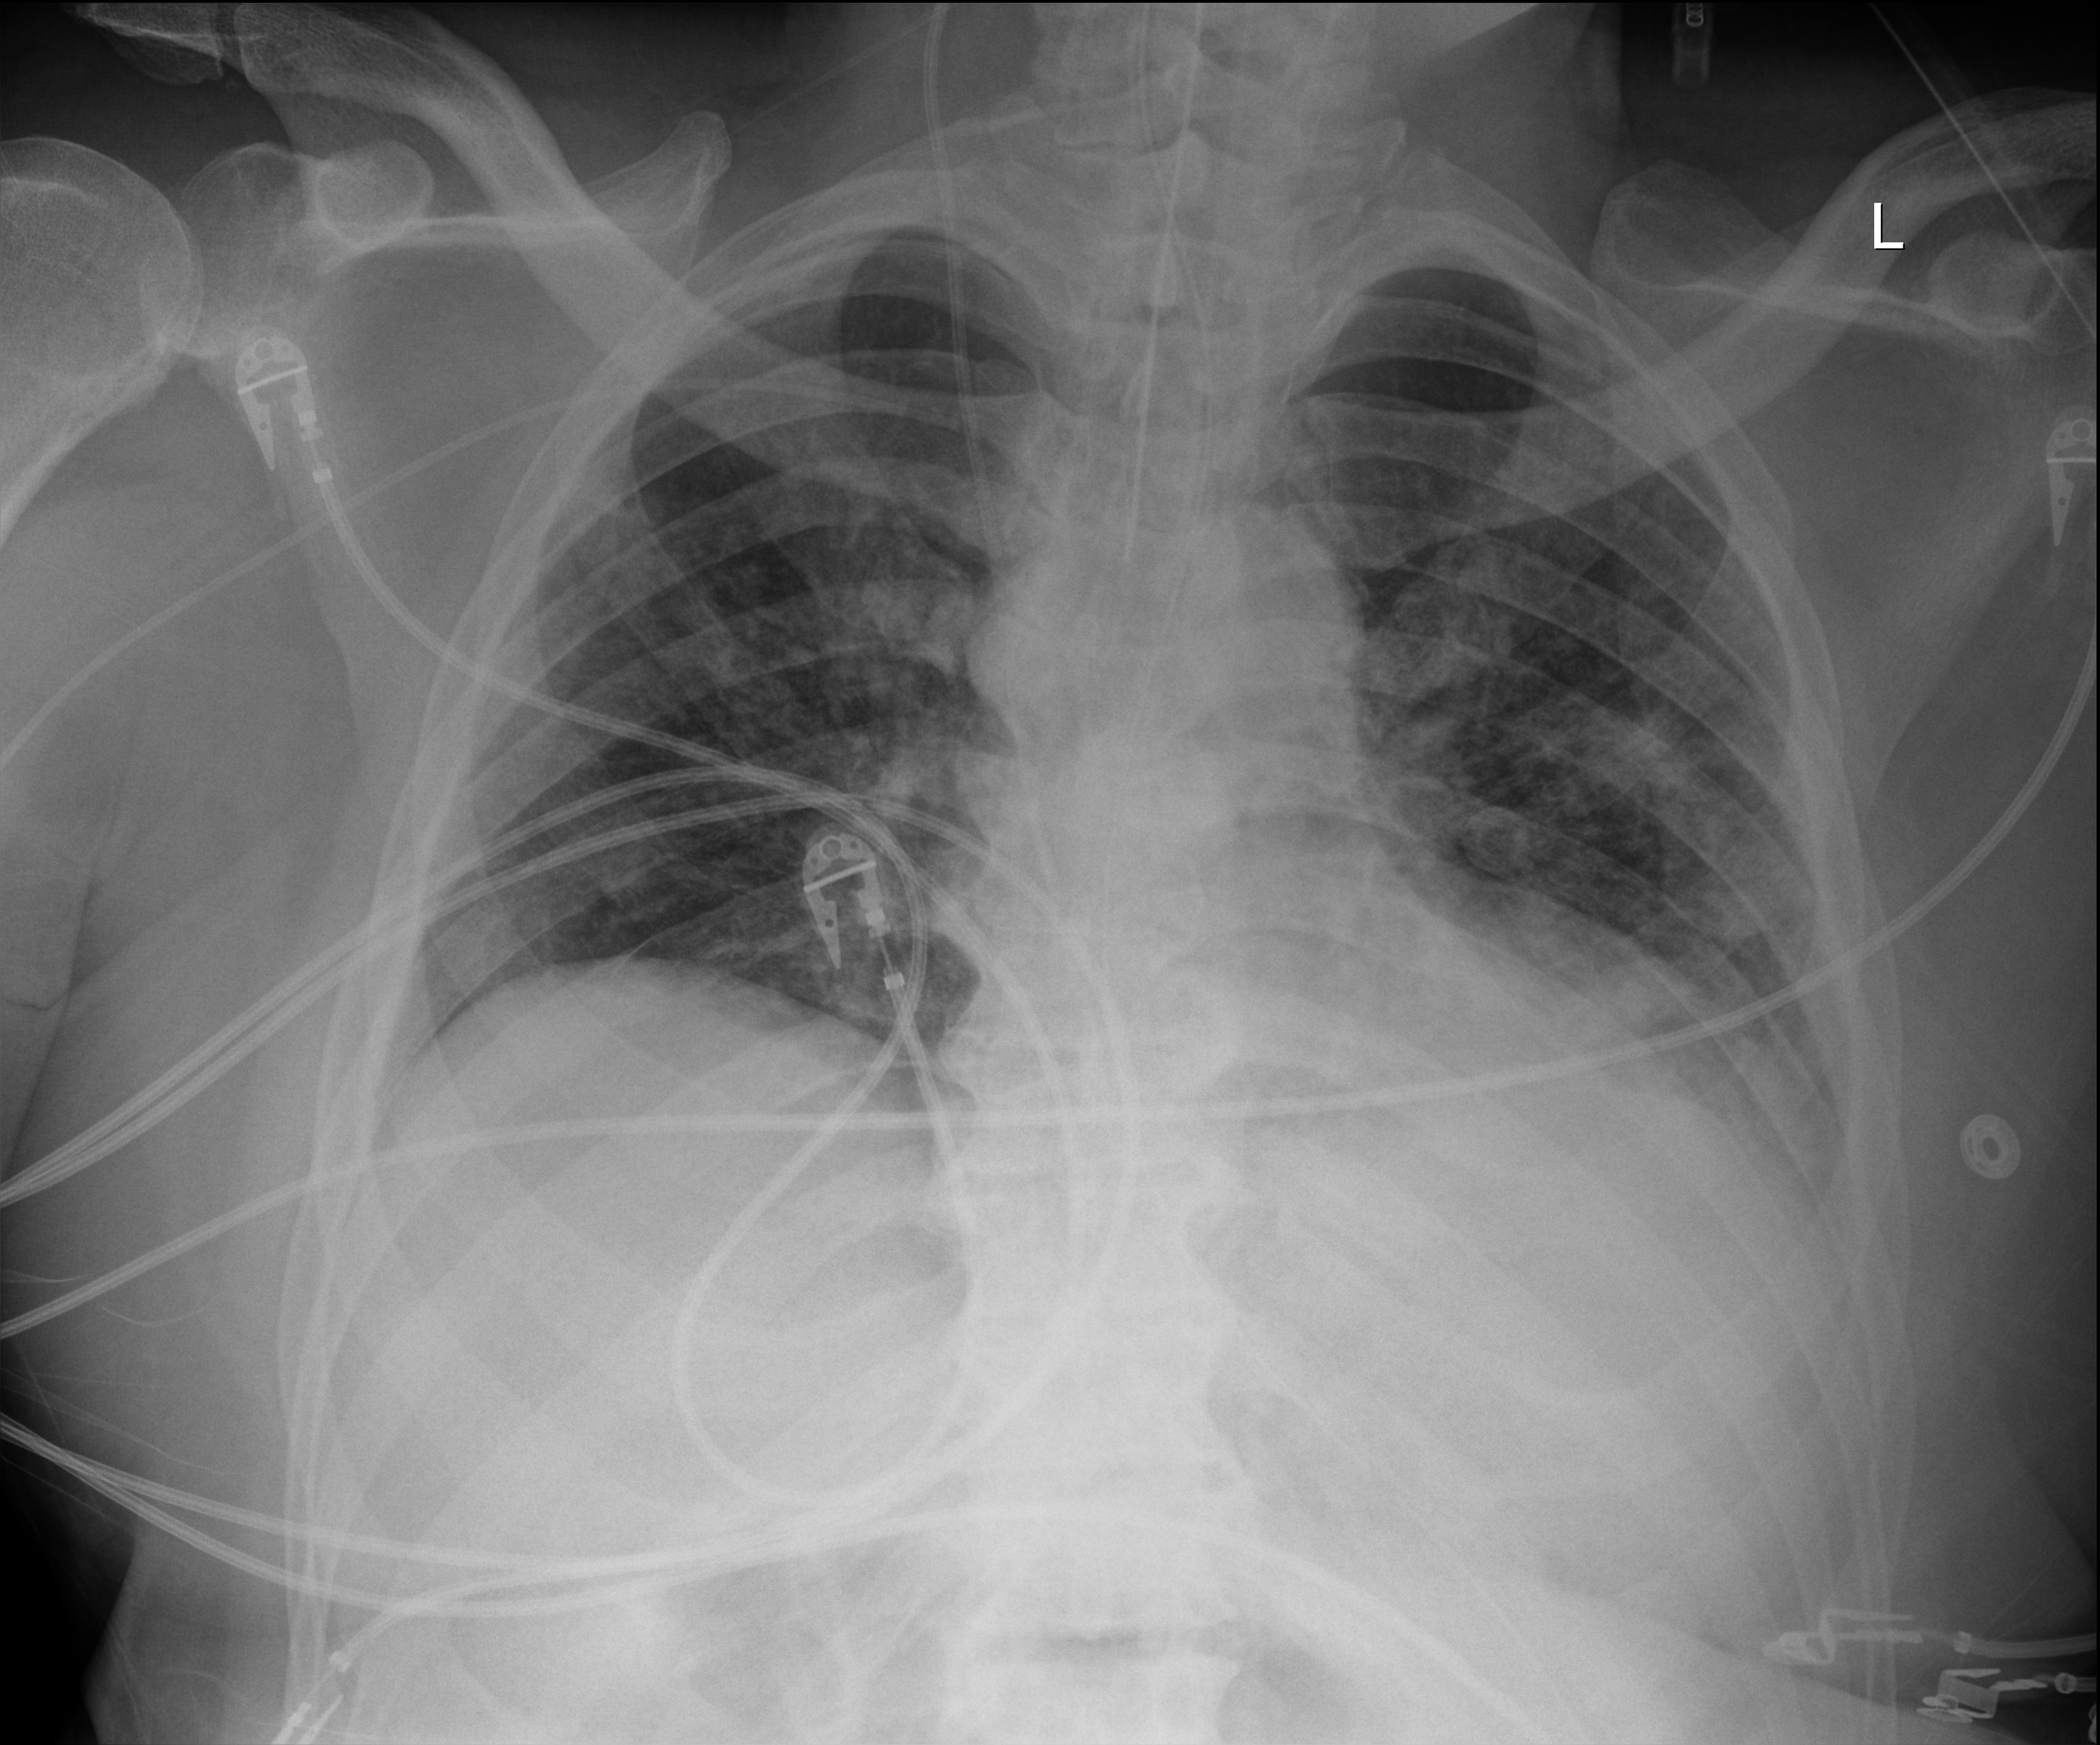
Bedside chest radiograph (digital radiography), anteroposterior (AP) projection. Patient hospitalised with COVID-19; male, aged 18–59 years.
Hospital-stay facts (about this admission, not read from this image; timing relative to this image not recorded): hypertension (admission record): no; admitted to intensive care during this hospital stay: yes; length of hospital stay: 41 days.